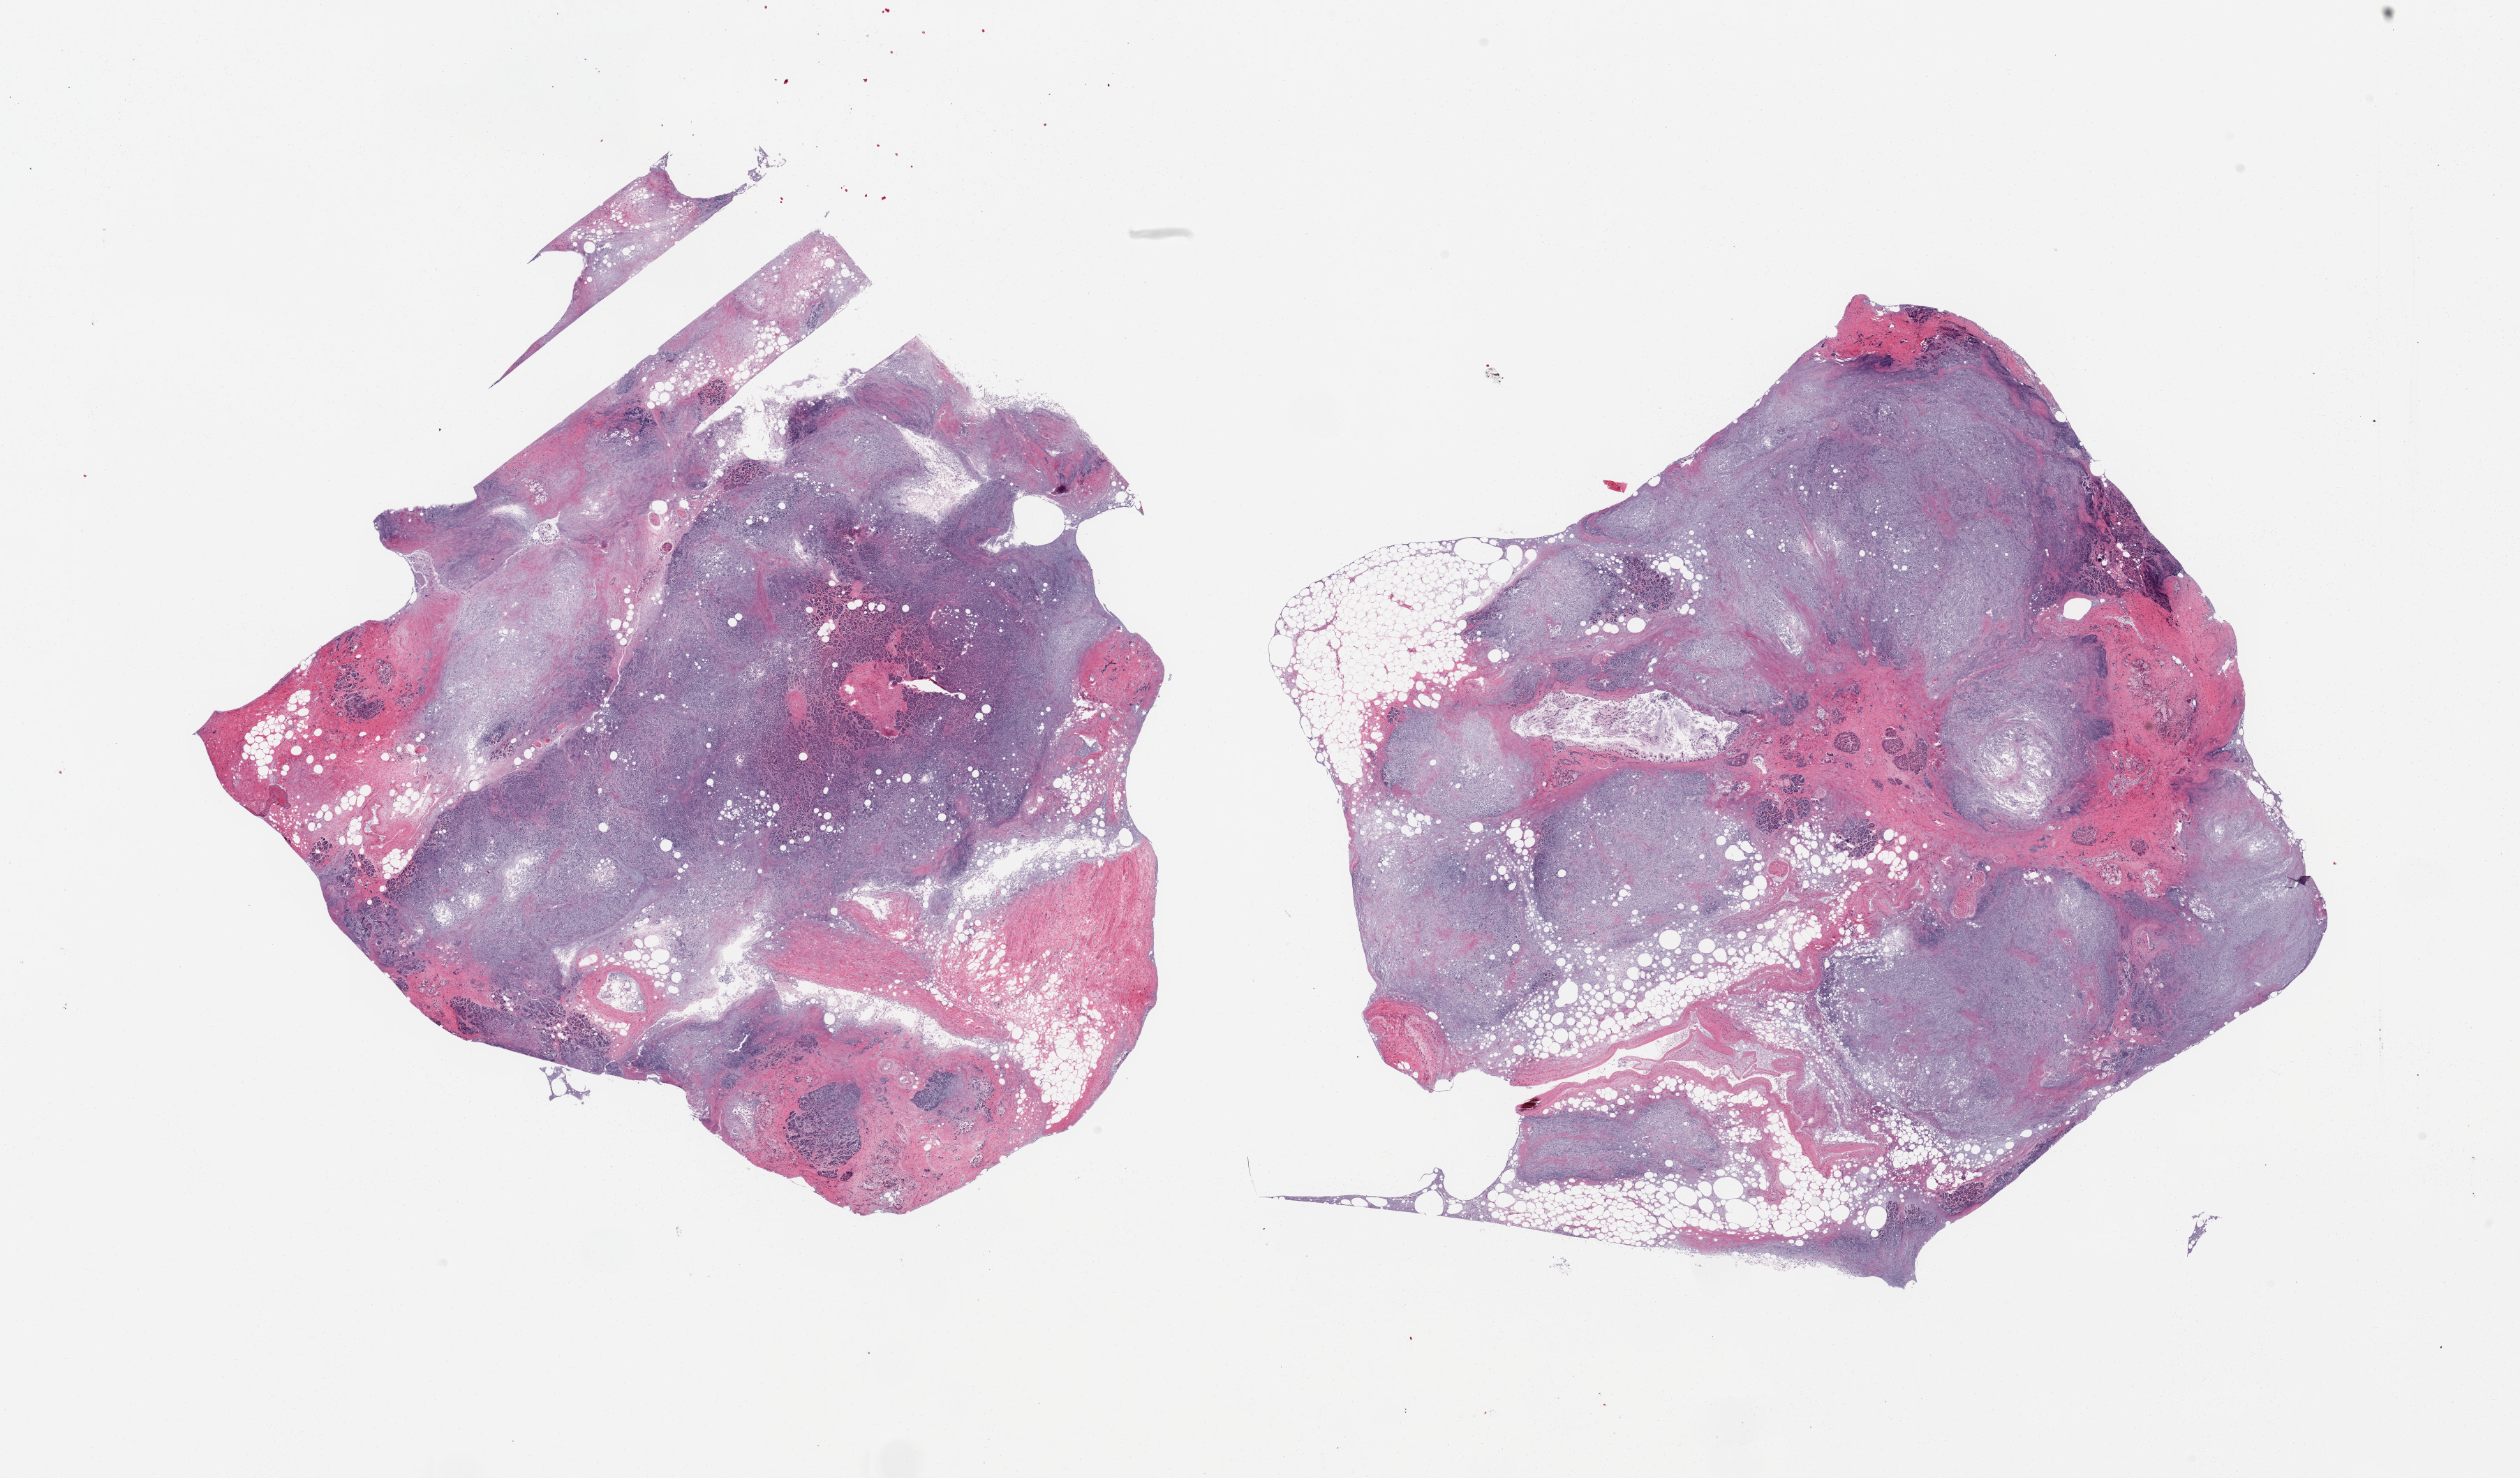
Whole-slide image, haematoxylin and eosin stain — a low-resolution overview of the entire scanned area, about 28.5 x 16.7 mm. PAXgene-fixed paraffin-embedded (PFPE) section. Sampled site (target tissue): pancreas. Donor tissue sample. Donor sex: male.
- reviewer comment on this tissue sample: 2 pieces, advance saponification; features suggest remote pancreatitis. Islets not discernable